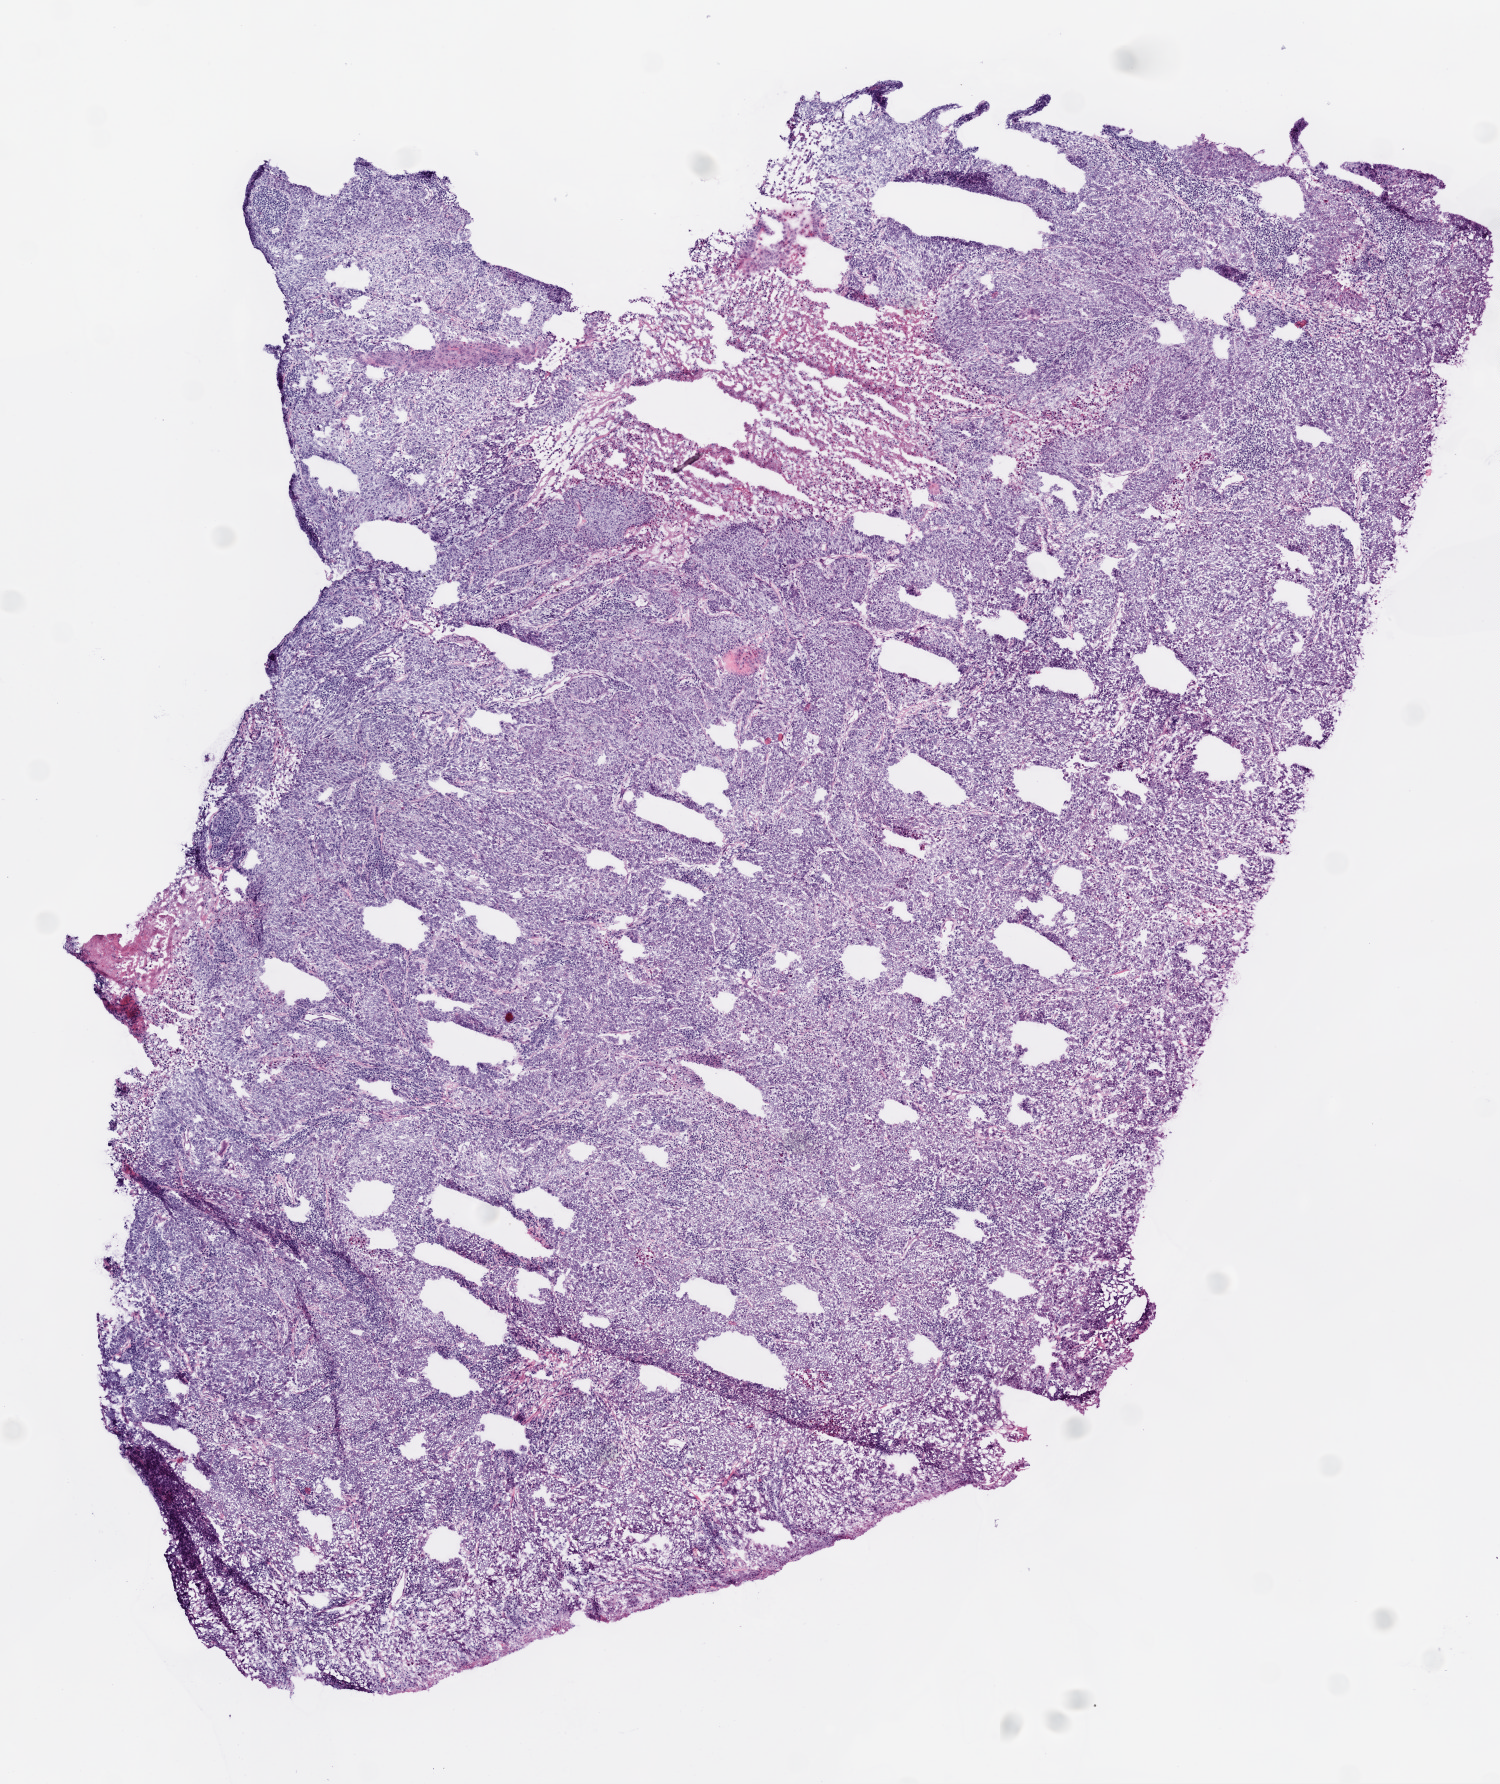
Digitized H&E-stained tissue section (whole slide) — a low-resolution overview of the entire scanned area, about 6.0 x 7.2 mm (from a 20x scan). Frozen section from the top of the tissue portion. Sample: primary tumour, lung. Male, age 73 years at initial diagnosis. Slide review estimates, as recorded: tumour cells 87%, tumour nuclei 80%.
Diagnosis: Squamous cell carcinoma, NOS (lower lobe, lung).